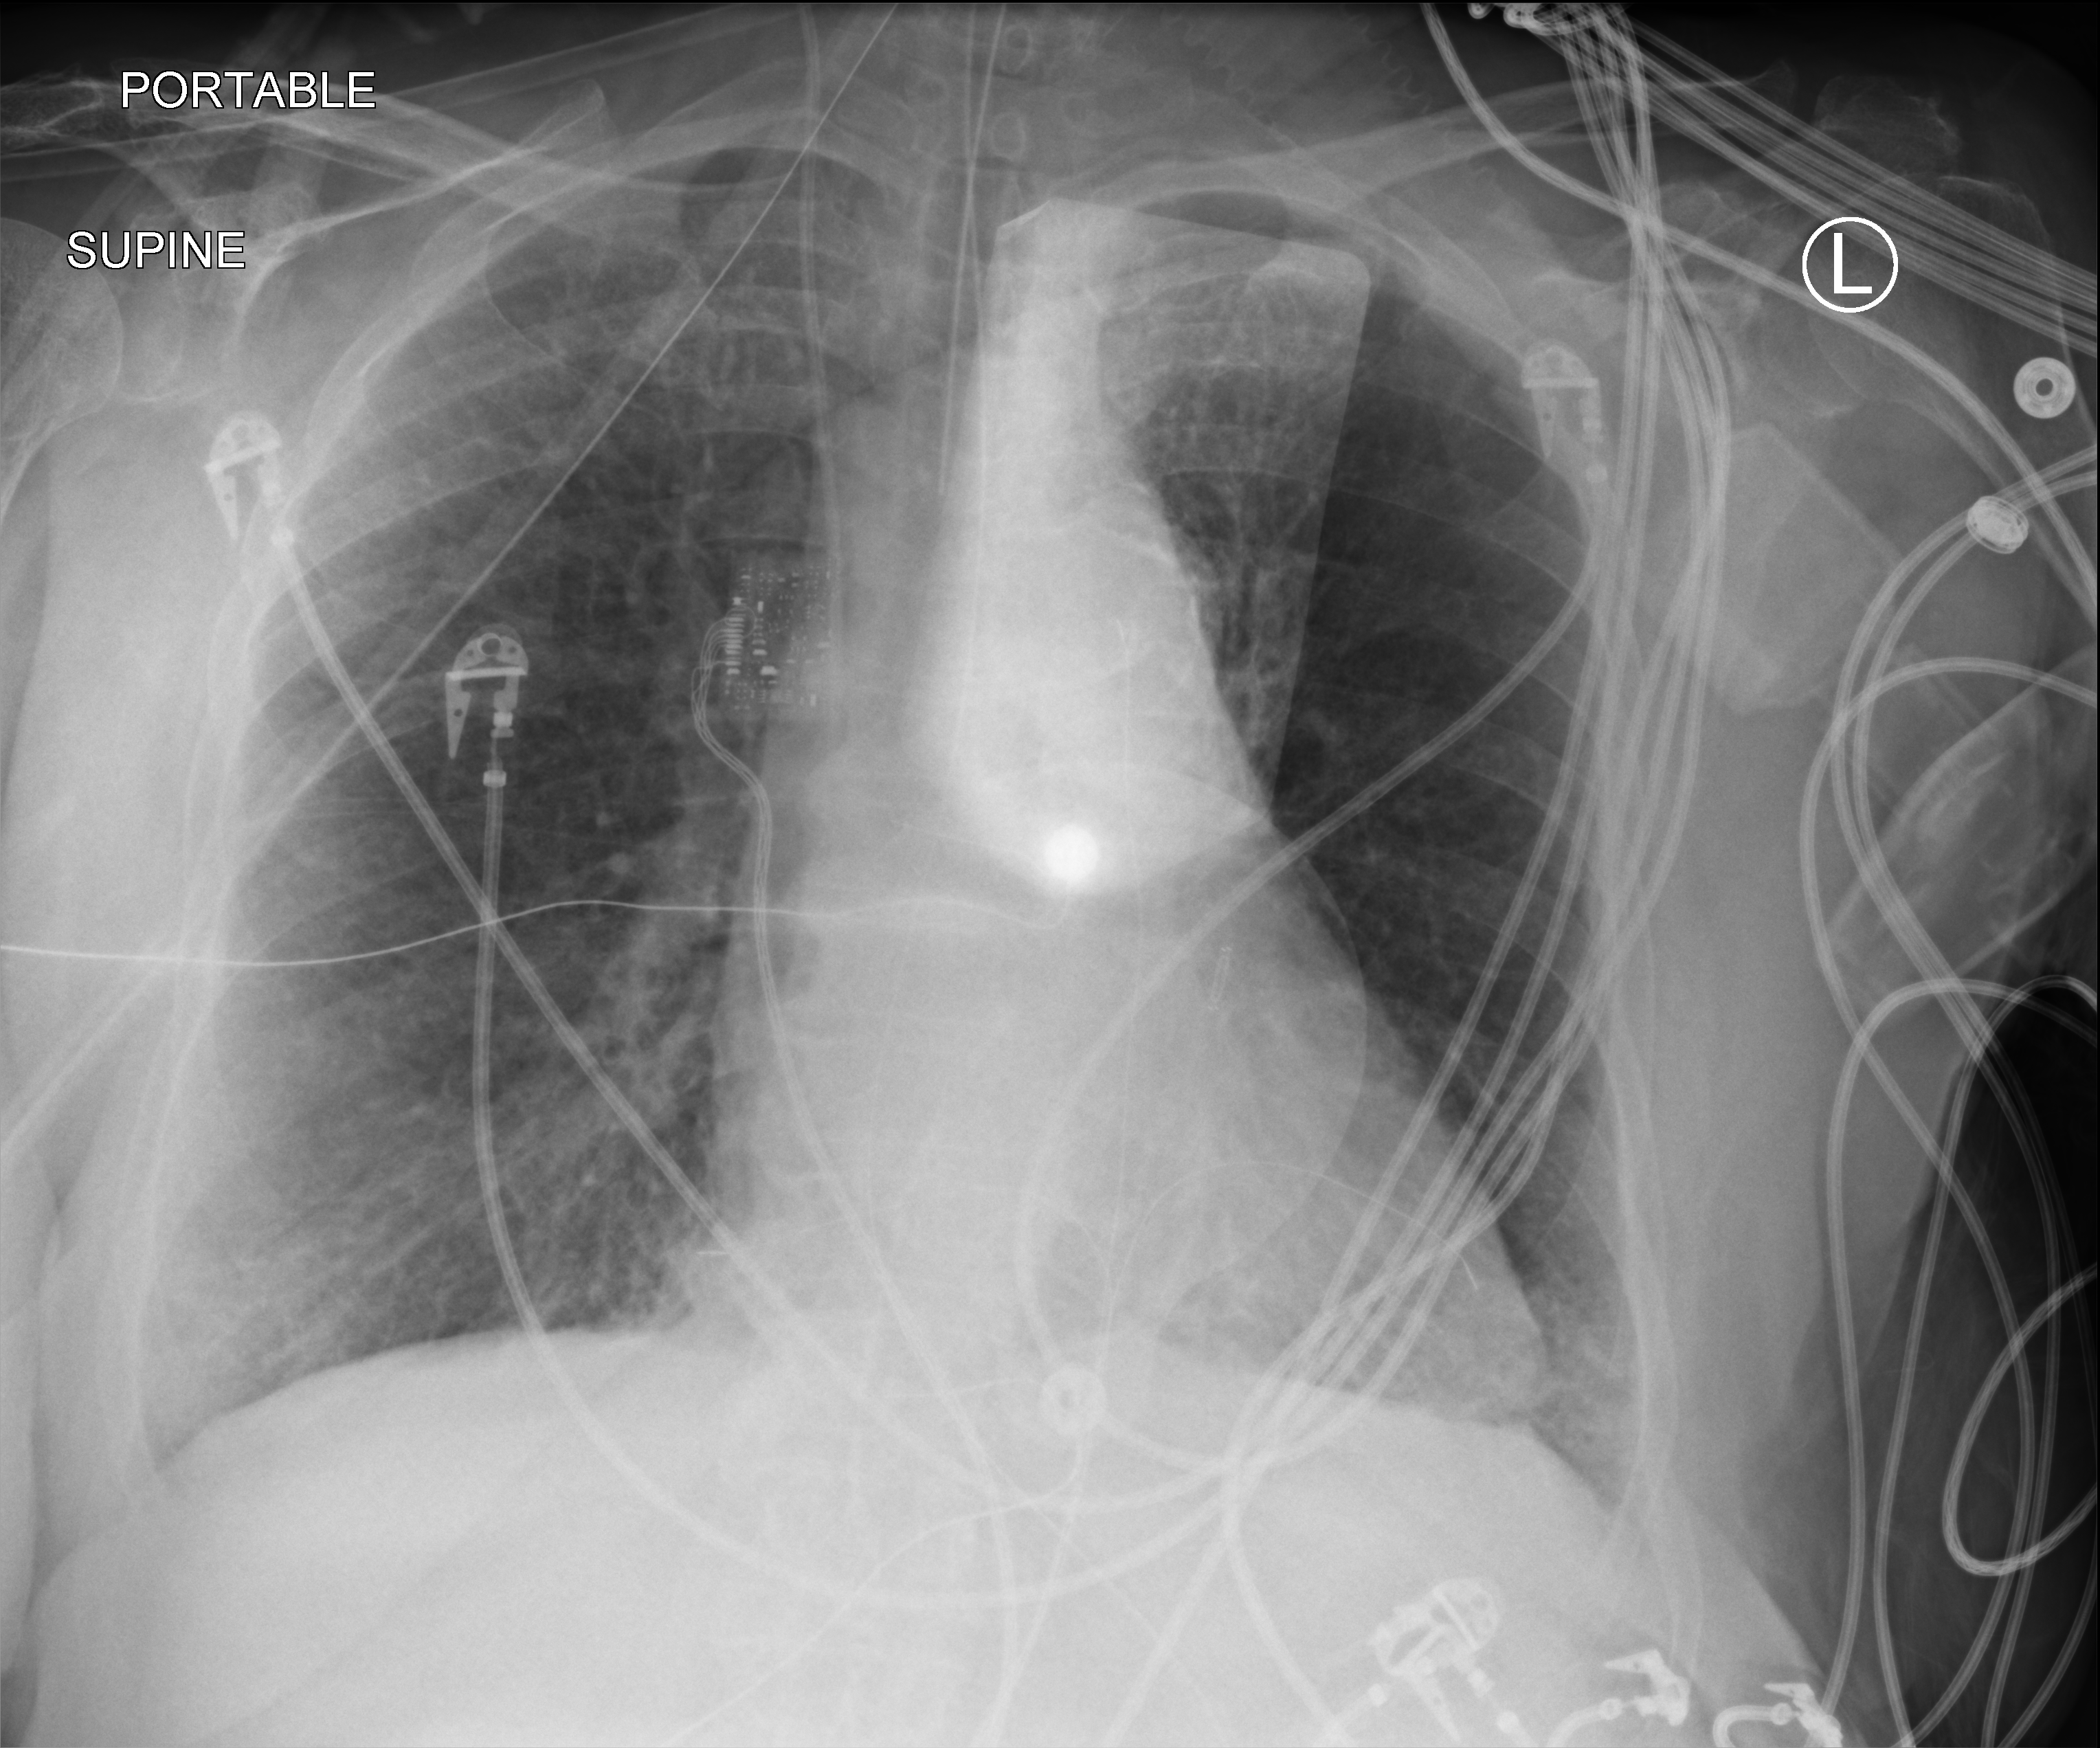
Bedside chest radiograph (computed radiography), anteroposterior (AP) projection. Patient hospitalised with COVID-19; female, aged 75–90 years.
Hospital-stay facts (about this admission, not read from this image; timing relative to this image not recorded): mechanically ventilated during this hospital stay: yes; other chronic lung disease (admission record): no.